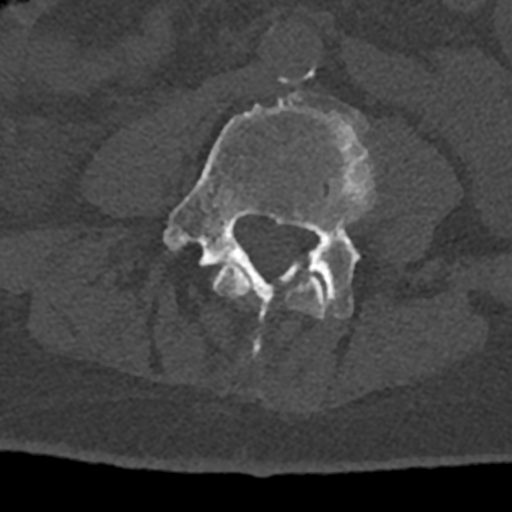
CT including the spine, one axial slice; 120 kVp; bone window (W 1800 / L 400 HU); 0.5 mm slice thickness; 512 × 512 image matrix, field of view 160 × 160 mm. Patient: male, 74 years. From the clinical record (not read from this slice): primary cancer: renal.
Structures marked on this image (semi-automatic segmentation, software-assisted and operator-edited):
- L3 vertebra: bounding box (x1, y1, x2, y2) in pixels: (212, 263, 327, 319)
- L4 vertebra: (163, 83, 375, 355)